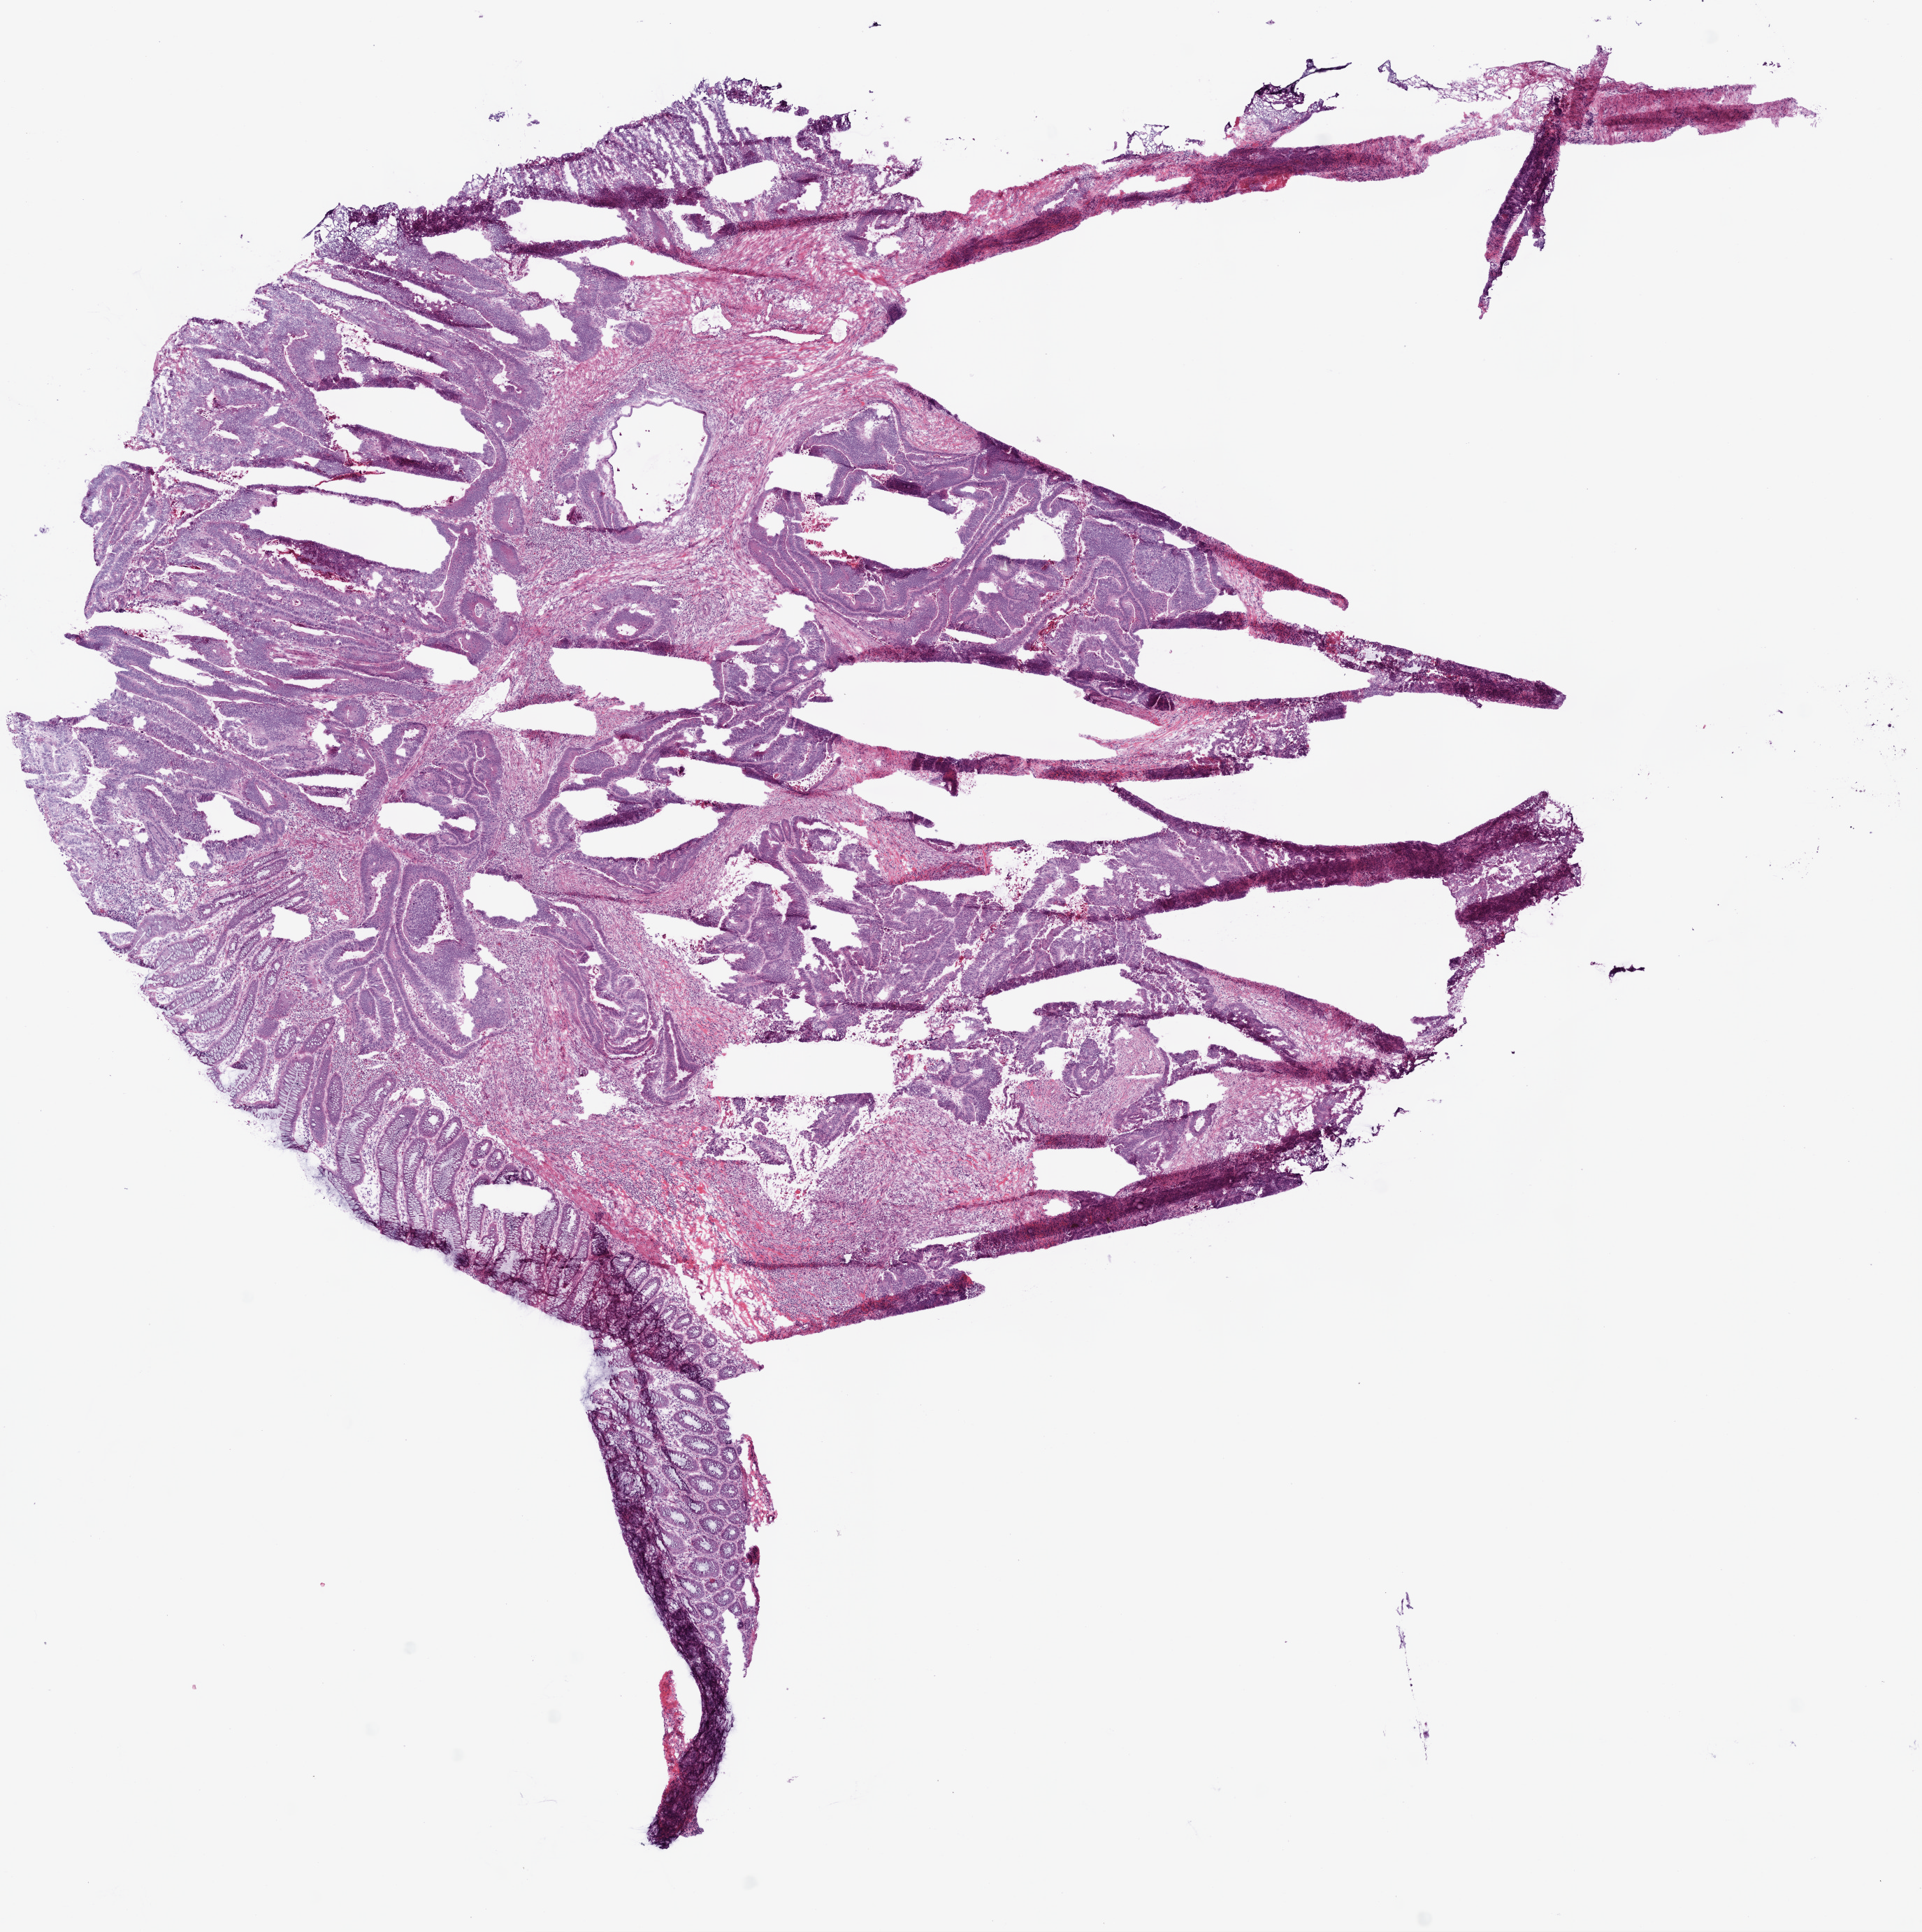
Digitized Hematoxylin and eosin (H&E) stained tissue section (whole slide), low-resolution overview of the scanned area, about 11.0 x 11.1 mm (from a 20x scan), frozen section from the bottom of the tissue portion, rectum, primary tumour sample. Male, age 63 years at initial diagnosis. Pathologist review of this section (percent, as recorded): tumour cells 75%, tumour nuclei 75%, normal cells 10%, stromal cells 10%, necrosis 5%.
- AJCC pathologic stage: I
- lymph nodes positive (case pathology): 0 of 33 examined
- histologic diagnosis: Adenocarcinoma, NOS (rectosigmoid junction)